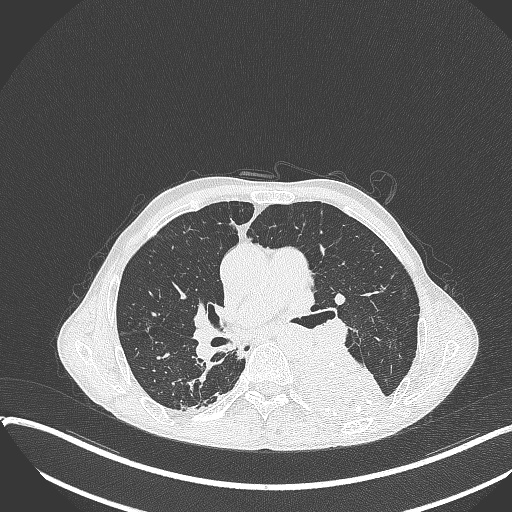
Chest CT, one axial slice; slice 215 of 401 in the series (ordered by position); lung window (W 1500 / L -600 HU); 1 mm slice thickness; 512 × 512 image matrix, field of view 400 × 400 mm. Patient: male, 57 years. Case-level facts recorded for this patient, not image findings: clinical TNM (as recorded): T4 N0 M0.
Structures marked on this image (bounding box drawn by a radiologist):
- lung tumour (recorded histology: squamous cell carcinoma): box from (x=289, y=348) to (x=390, y=423) px